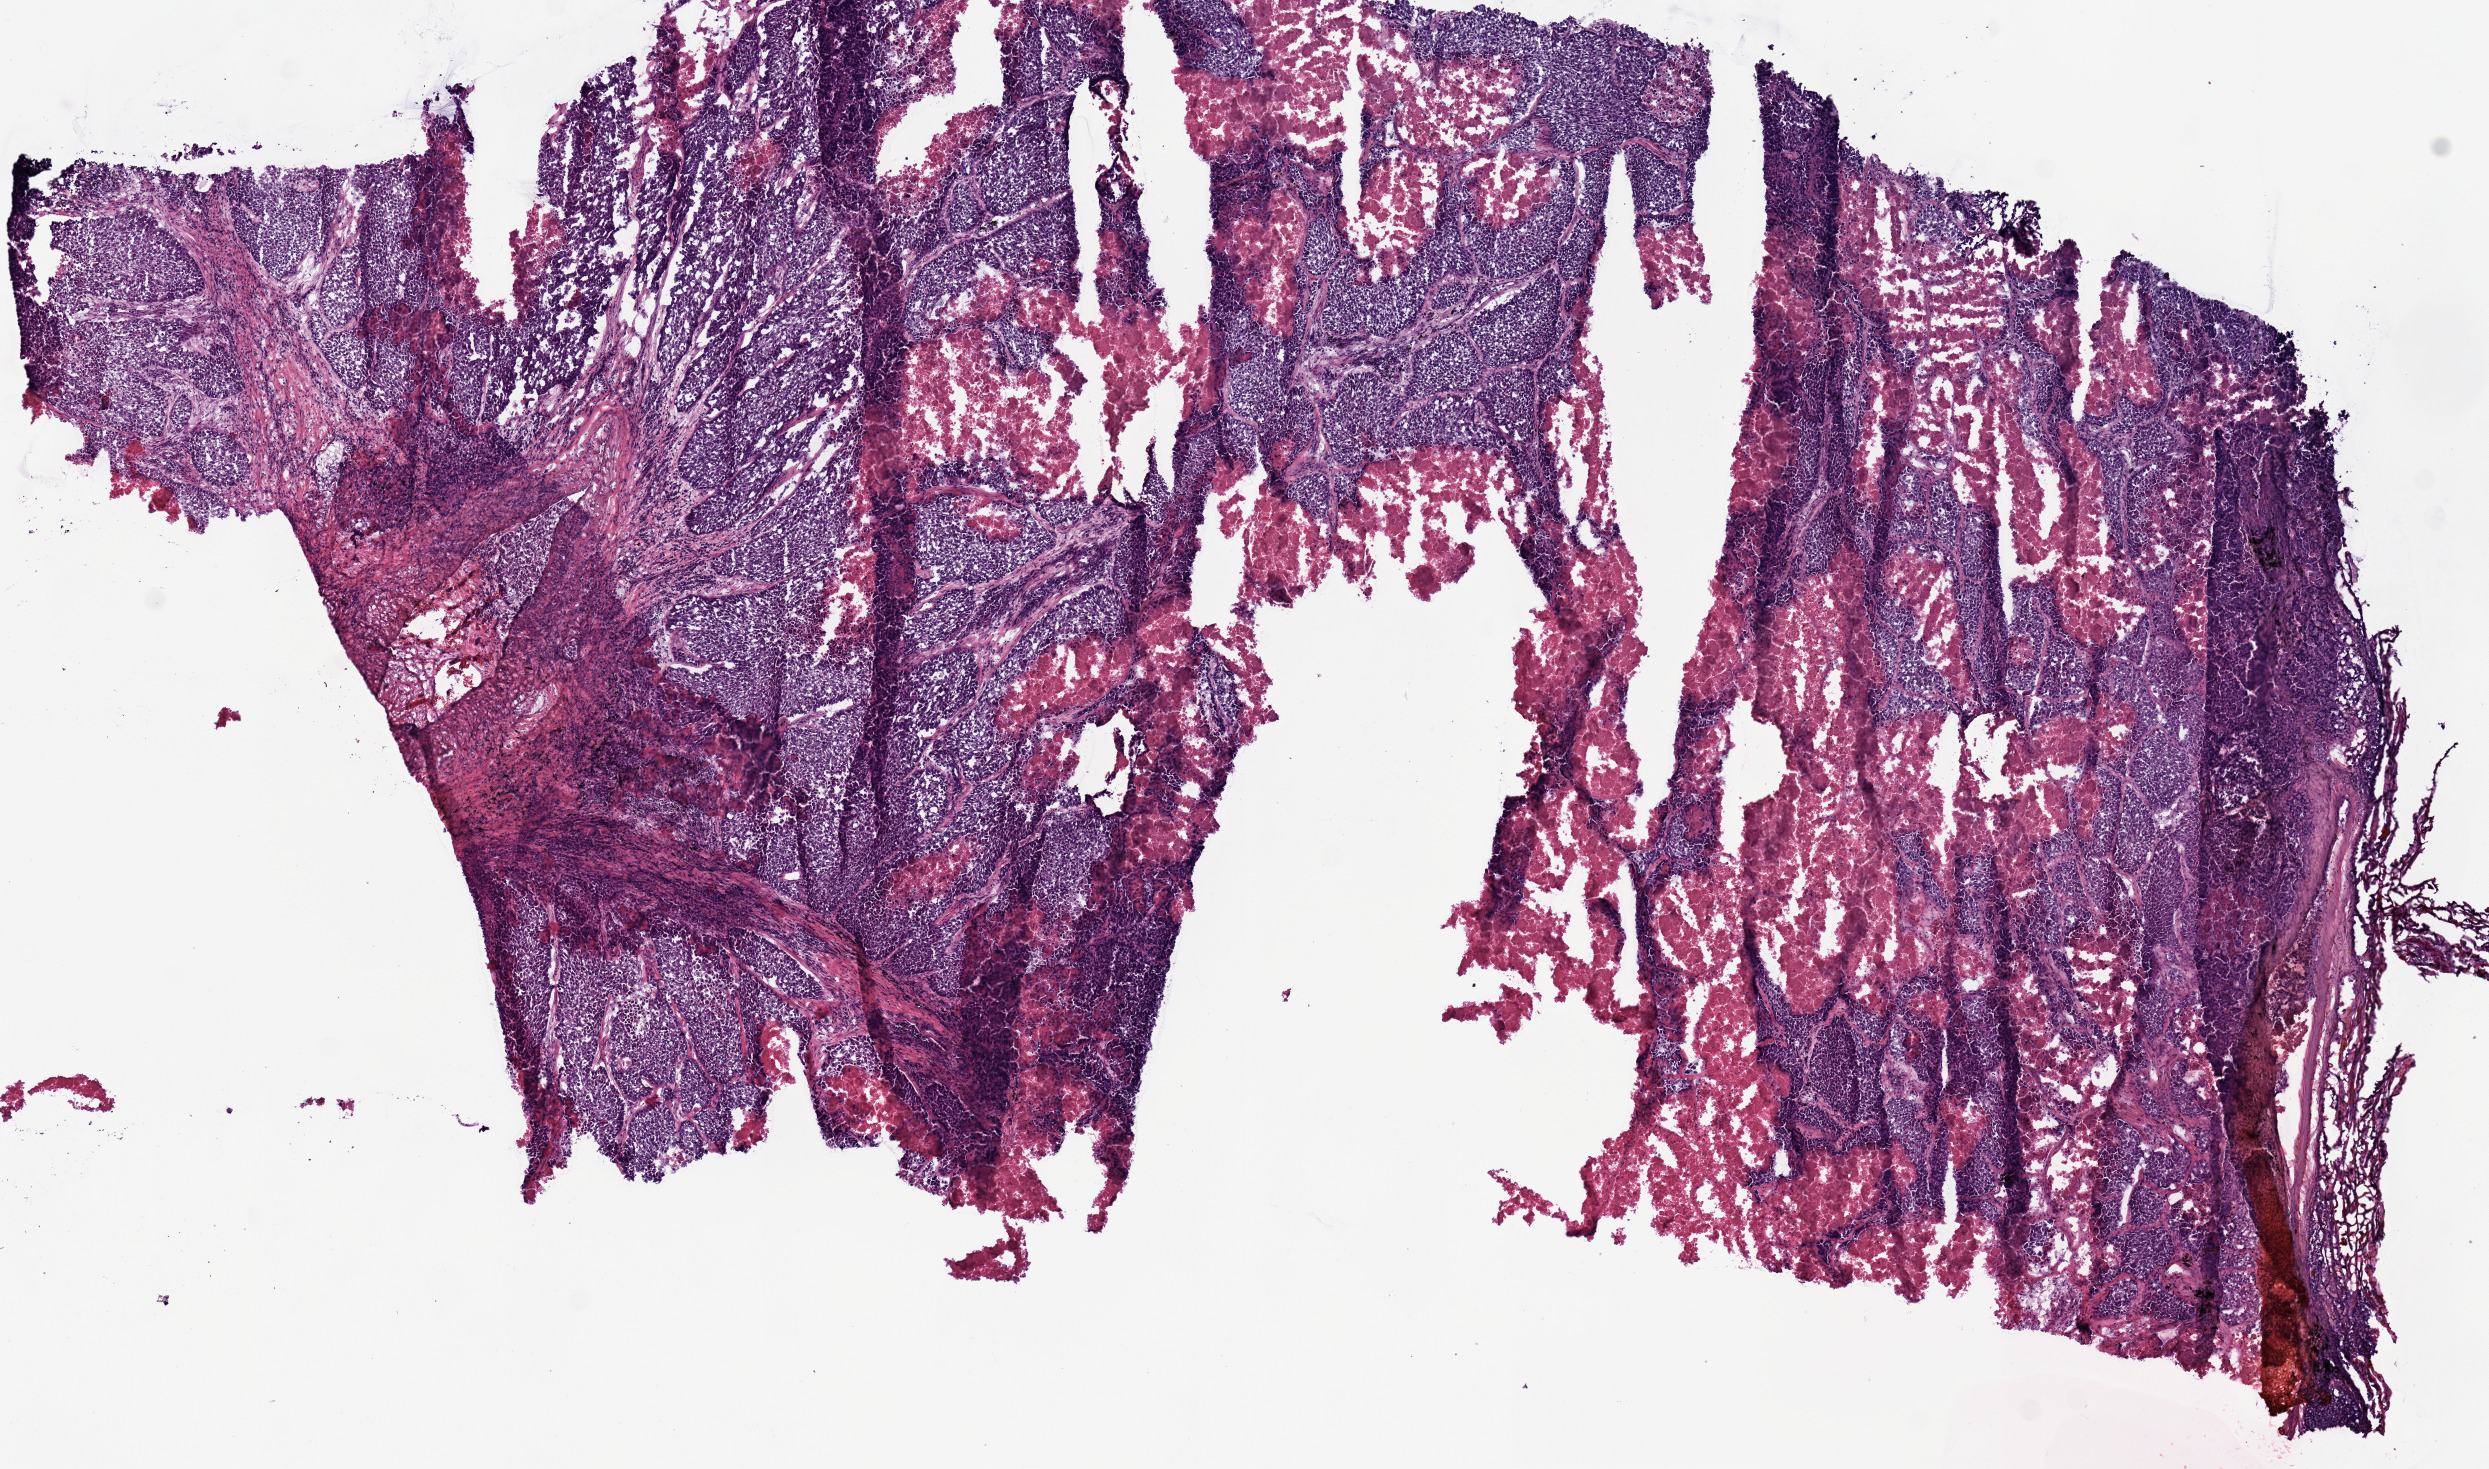
Whole-slide histology image, H&E, shown as a low-resolution overview of the whole scanned area (about 9.8 x 5.8 mm, acquisition: 20x scan), frozen section, lung, primary tumour sample. Male, age 71 years at initial diagnosis. Slide review estimates, as recorded: tumour cells 82%, tumour nuclei 85%, normal cells 0%, stromal cells 10%, necrosis 8%.
AJCC pathologic stage: IB. Laterality: left. Pathologic diagnosis: Squamous cell carcinoma, NOS (upper lobe, lung). TNM: T2 N0 M0.